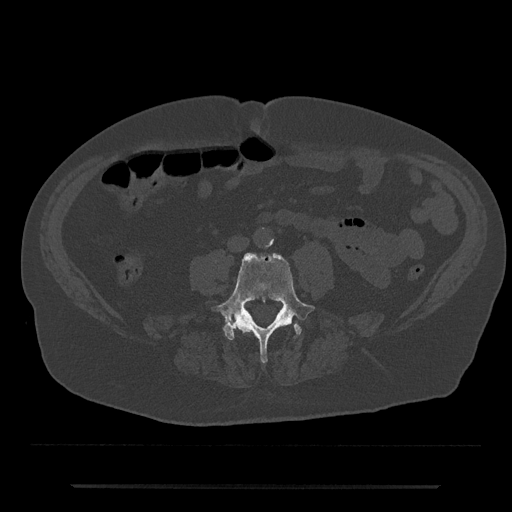
CT including the spine, one axial slice; slice 351 of 797 in the series (ordered by position); reconstruction kernel Br40s/3; bone window (W 1800 / L 400 HU); 0.5 mm slice thickness; 512 × 512 image matrix, field of view 434 × 434 mm. Patient: male, 80 years. Case-level facts recorded for this patient, not image findings: primary cancer: prostate.
Outlined on this slice (semi-automatically segmented with operator editing):
- L4 vertebra: box from (x=211, y=253) to (x=316, y=363) px